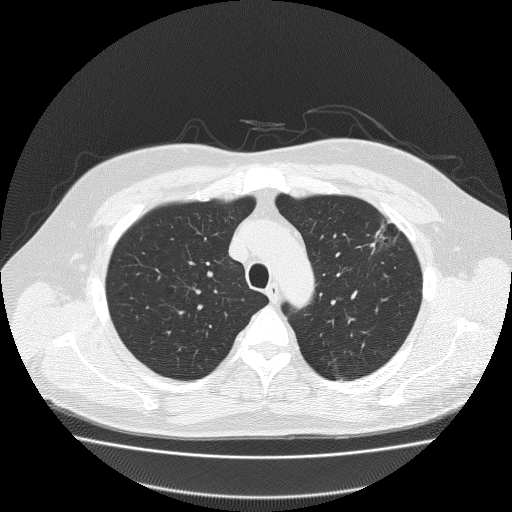
Low-dose screening chest CT, one axial slice; position 157 of 204 along the scan axis; reconstruction kernel FC51; 120 kVp; lung window (W 1500 / L -600 HU); 2 mm slice thickness; 512 × 512 image matrix.
Structures marked on this image (outlined manually by an expert reader):
- lesion 1 (tumor, upper lobe of left lung): box from (x=368, y=225) to (x=395, y=255) px